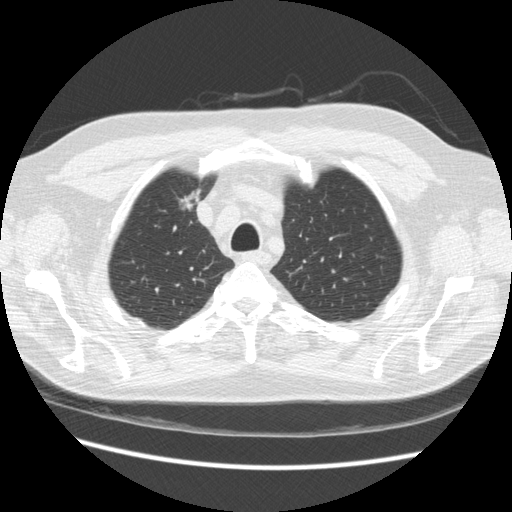
Chest CT (low-dose screening protocol), one axial image. Third screening round (two years after baseline). Lung window (W 1500 / L -600 HU). 512 × 512 image matrix. Male, age 66 years at enrolment. Former smoker at enrolment.
Expert reader's lesion annotation, bounding box <166,180,211,220> (left, top, right, bottom; pixels). Screening reader's record for this exam: no non-calcified nodule ≥4 mm recorded. Lung cancer was diagnosed 229 days after this screen: bronchiolo-alveolar adenocarcinoma, NOS, right upper lobe, moderately differentiated (G2), stage IA (AJCC 6th edition), 12 mm at pathology.